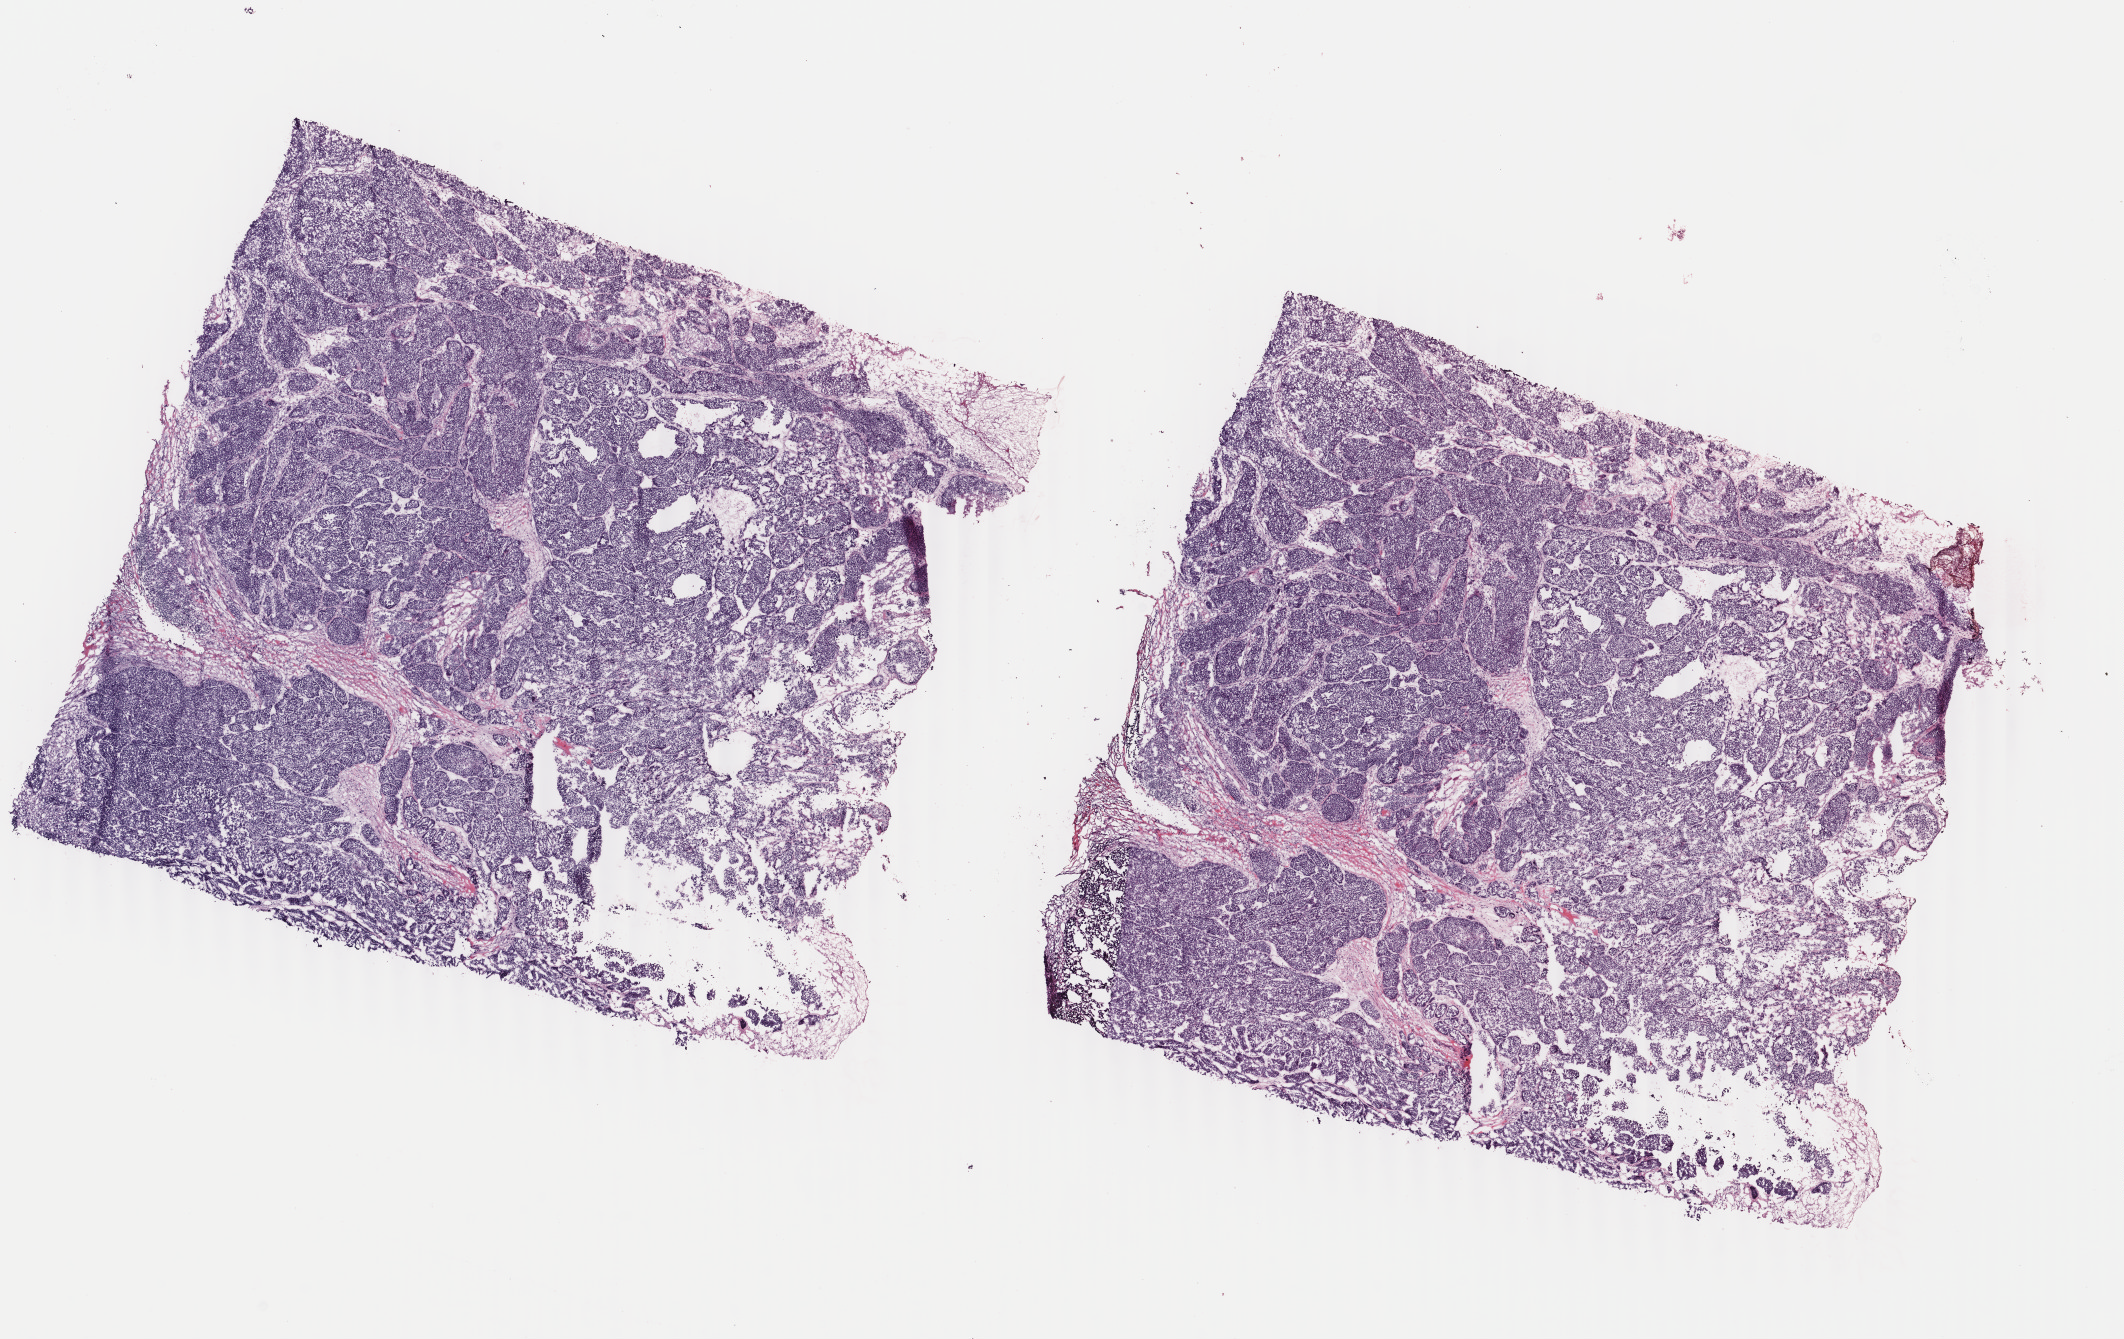
H&E whole-slide image, whole scanned area (about 16.9 x 10.7 mm, slide scanned at 40x) shown as a low-resolution overview, frozen section from the top of the tissue portion, breast, primary tumour sample. Female patient; age at initial diagnosis 43 years. Pathologist review of this section (percent, as recorded): tumour cells 90%, tumour nuclei 80%, normal cells 0%, stromal cells 10%, necrosis 0%. Inflammatory infiltration, as recorded: lymphocyte infiltration 0%, monocyte infiltration 0%, neutrophil infiltration 0%.
Lymph nodes positive (case pathology): 0 of 5 examined. AJCC pathologic stage: IIA. Pathologic diagnosis: Infiltrating duct carcinoma, NOS. Laterality: left.